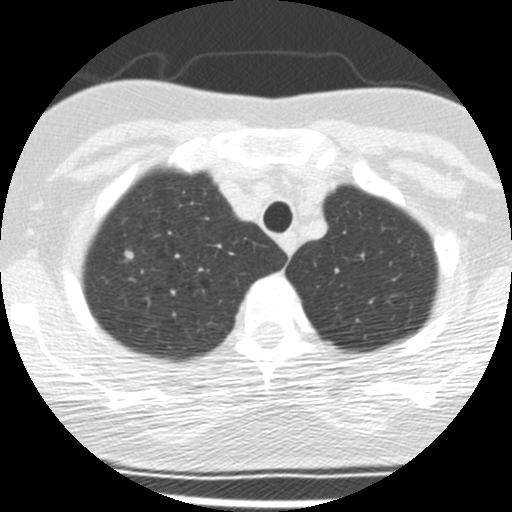
Axial slice from a low-dose chest CT screening exam; first (baseline) screen; lung window (W 1500 / L -600 HU); 2.5 mm slice thickness; slice 36 of 190 in the series; 512 × 512 image matrix. Female, age 56 years at enrolment. Current smoker at enrolment.
Expert reader's lesion annotation, box from (x=107, y=235) to (x=148, y=273) px. The exam's reader record, not a measurement of the box and not confirmed to be the same lesion: non-calcified nodule or mass ≥4 mm, right upper lobe, 6 × 6 mm, smooth margins, soft tissue attenuation. Lung cancer was diagnosed 281 days after this screen: small cell carcinoma, NOS, right upper lobe, stage IIIB (AJCC 6th edition).